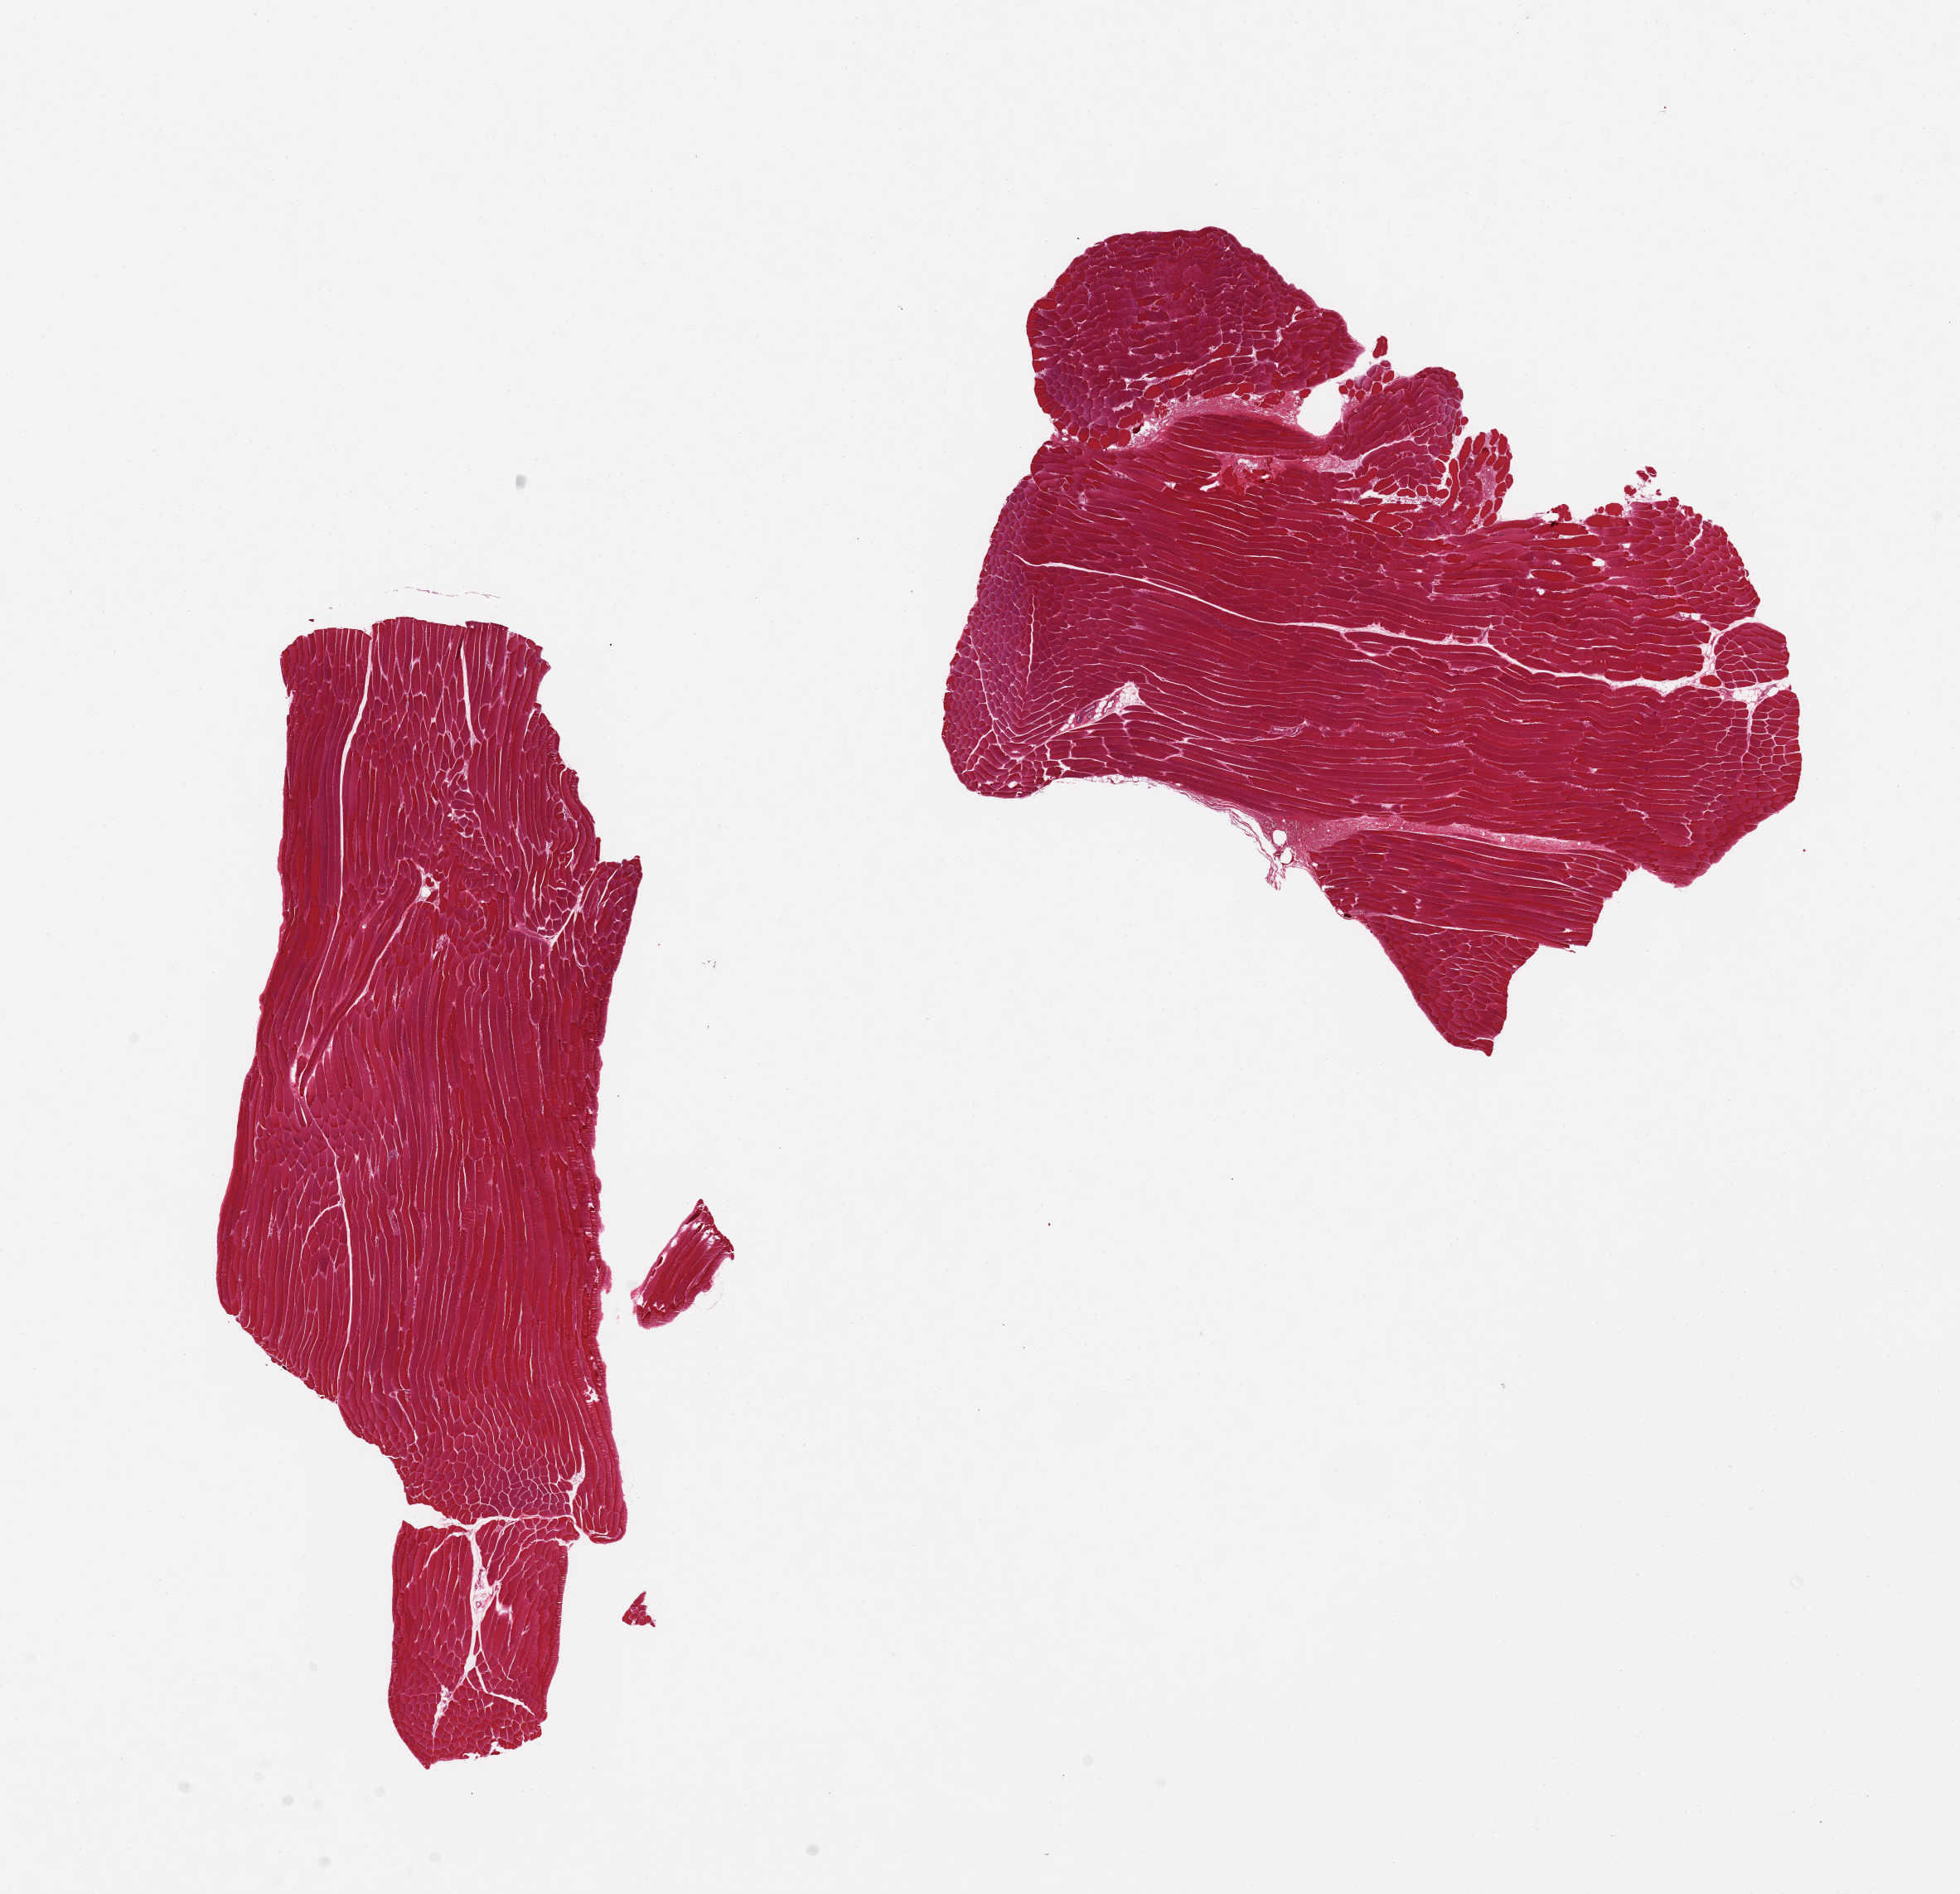
Whole-slide image, hematoxylin and eosin (H&E) stain, brightfield, low-resolution overview of the scanned area, about 18.7 x 18.1 mm (from a 20x scan), PAXgene-fixed, paraffin-embedded tissue, section of skeletal muscle (target tissue), tissue donor sample. Male donor.
Review note (as recorded): 2 pieces.